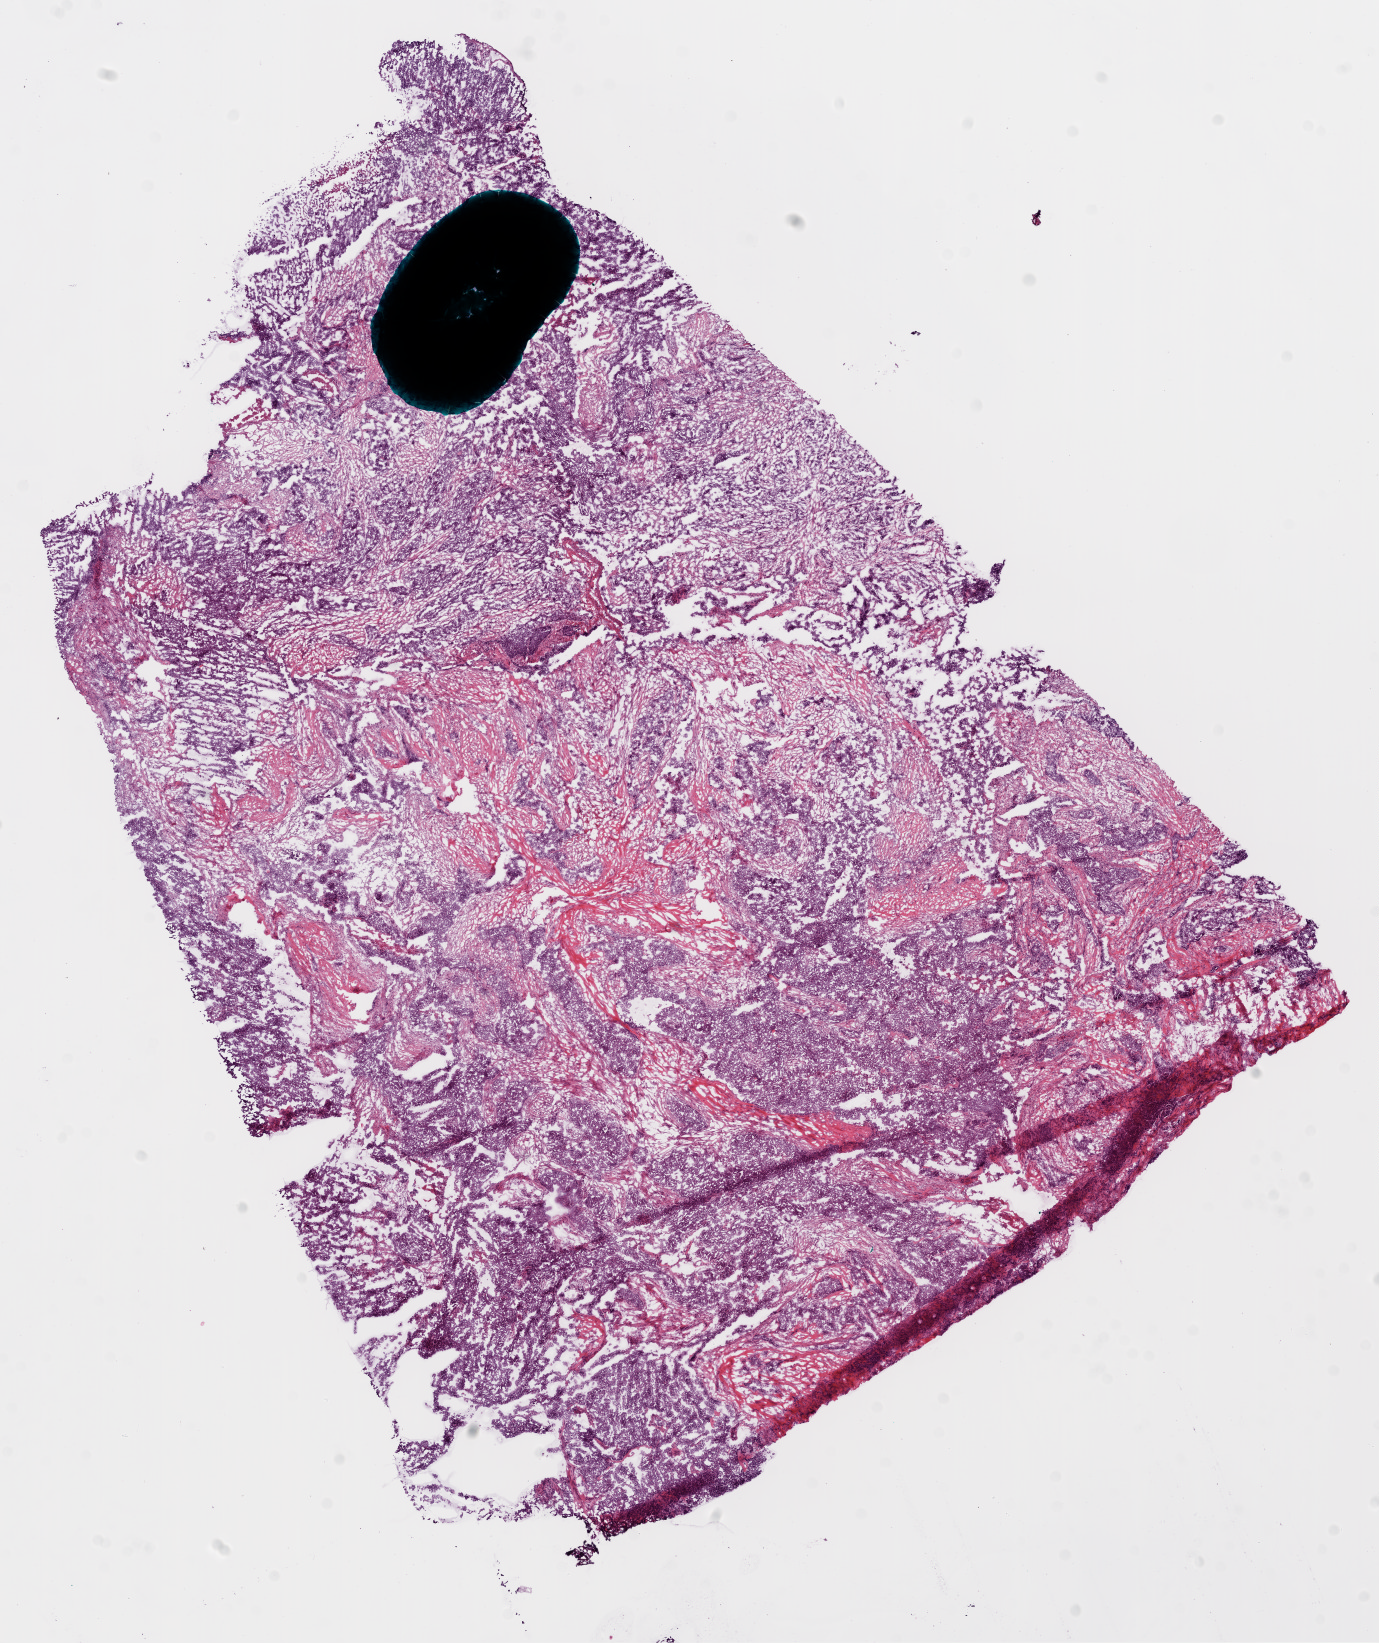
H&E-stained whole-slide image, whole scanned area (about 11.1 x 13.2 mm, slide scanned at 20x) shown as a low-resolution overview. Frozen section from the bottom of the tissue portion. Ovary, primary tumour sample. Female, age 64 years at initial diagnosis. Composition of this section per pathologist review: tumour cells 65%, tumour nuclei 90%, normal cells 0%, stromal cells 30%, necrosis 5%.
FIGO stage: IIIC. Histologic diagnosis: Serous cystadenocarcinoma, NOS.